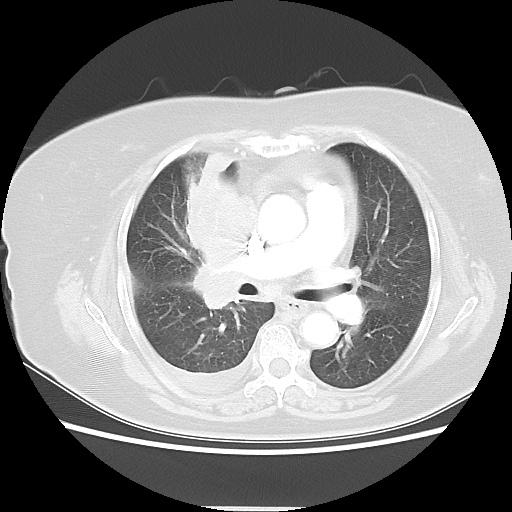
Chest CT, one axial slice; slice 28 of 48 in the series (ordered by position); 120 kVp; lung window (W 1500 / L -600 HU); 5 mm slice thickness; 512 × 512 image matrix, field of view 360 × 360 mm. Female patient, age 73 years. Case-level facts recorded for this patient, not image findings: clinical TNM (as recorded): T3 N3 M1b; histopathological grade: G3.
Annotated regions visible in this slice (rectangle marked by the reading radiologist):
- lung tumour (recorded histology: small cell carcinoma): box from (x=175, y=143) to (x=260, y=311) px